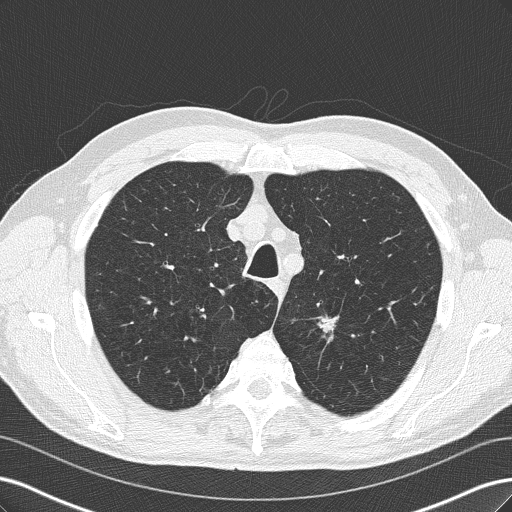
Low-dose screening chest CT, axial slice, third screening round (two years after baseline), lung window (W 1500 / L -600 HU), 2 mm slice thickness, slice 42 of 219 in the series. Male, age 66 years at enrolment. Current smoker at enrolment.
Lesion marked by an expert reader, bounding box [x1, y1, x2, y2] px = [296, 303, 352, 347]. The exam's reader record, not a measurement of the box and not confirmed to be the same lesion: non-calcified nodule or mass ≥4 mm, left upper lobe, 14 × 9 mm, spiculated (stellate) margins, soft tissue attenuation, pre-existing on the prior screen: yes; interval growth: yes. Official screen result: positive, other. Participant outcome: lung cancer diagnosed 19 days after this screen — squamous cell carcinoma, NOS, left upper lobe, poorly differentiated (G3), stage IA (AJCC 6th edition), 15 mm at pathology.